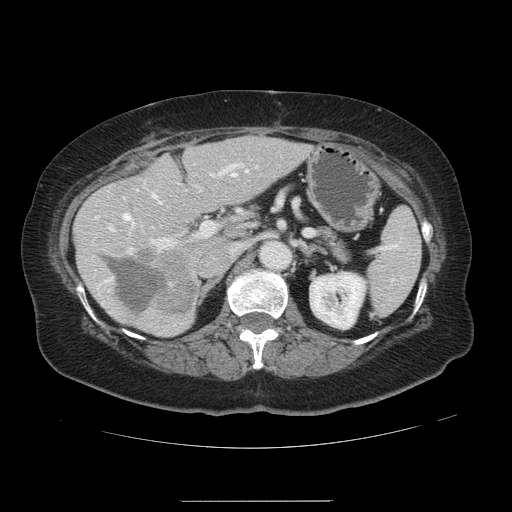
Contrast-enhanced abdominal CT, one axial slice. Position 72 of 141 along the scan axis. 120 kVp. Intravenous contrast given. Soft-tissue window (W 400 / L 40 HU). 2.5 mm slice thickness. 512 × 512 image matrix, field of view 393 × 393 mm. Female patient, age 74 years. Case-level facts recorded for this patient, not image findings: diagnosis: colorectal cancer liver metastases, imaged before liver resection; multiple liver metastases: yes; largest metastasis: 7 cm; disease in both lobes: yes.
Outlined on this slice (outlined manually by an expert reader):
- hepatic veins: bounding box (x1, y1, x2, y2) in pixels: (123, 173, 235, 230)
- liver: (75, 136, 306, 335)
- planned liver remnant (the part of the liver to remain after resection): (76, 136, 306, 335)
- portal vein (with intrahepatic branches): (109, 164, 248, 254)
- liver metastasis: (108, 259, 166, 314)
- liver metastasis: (136, 250, 195, 314)